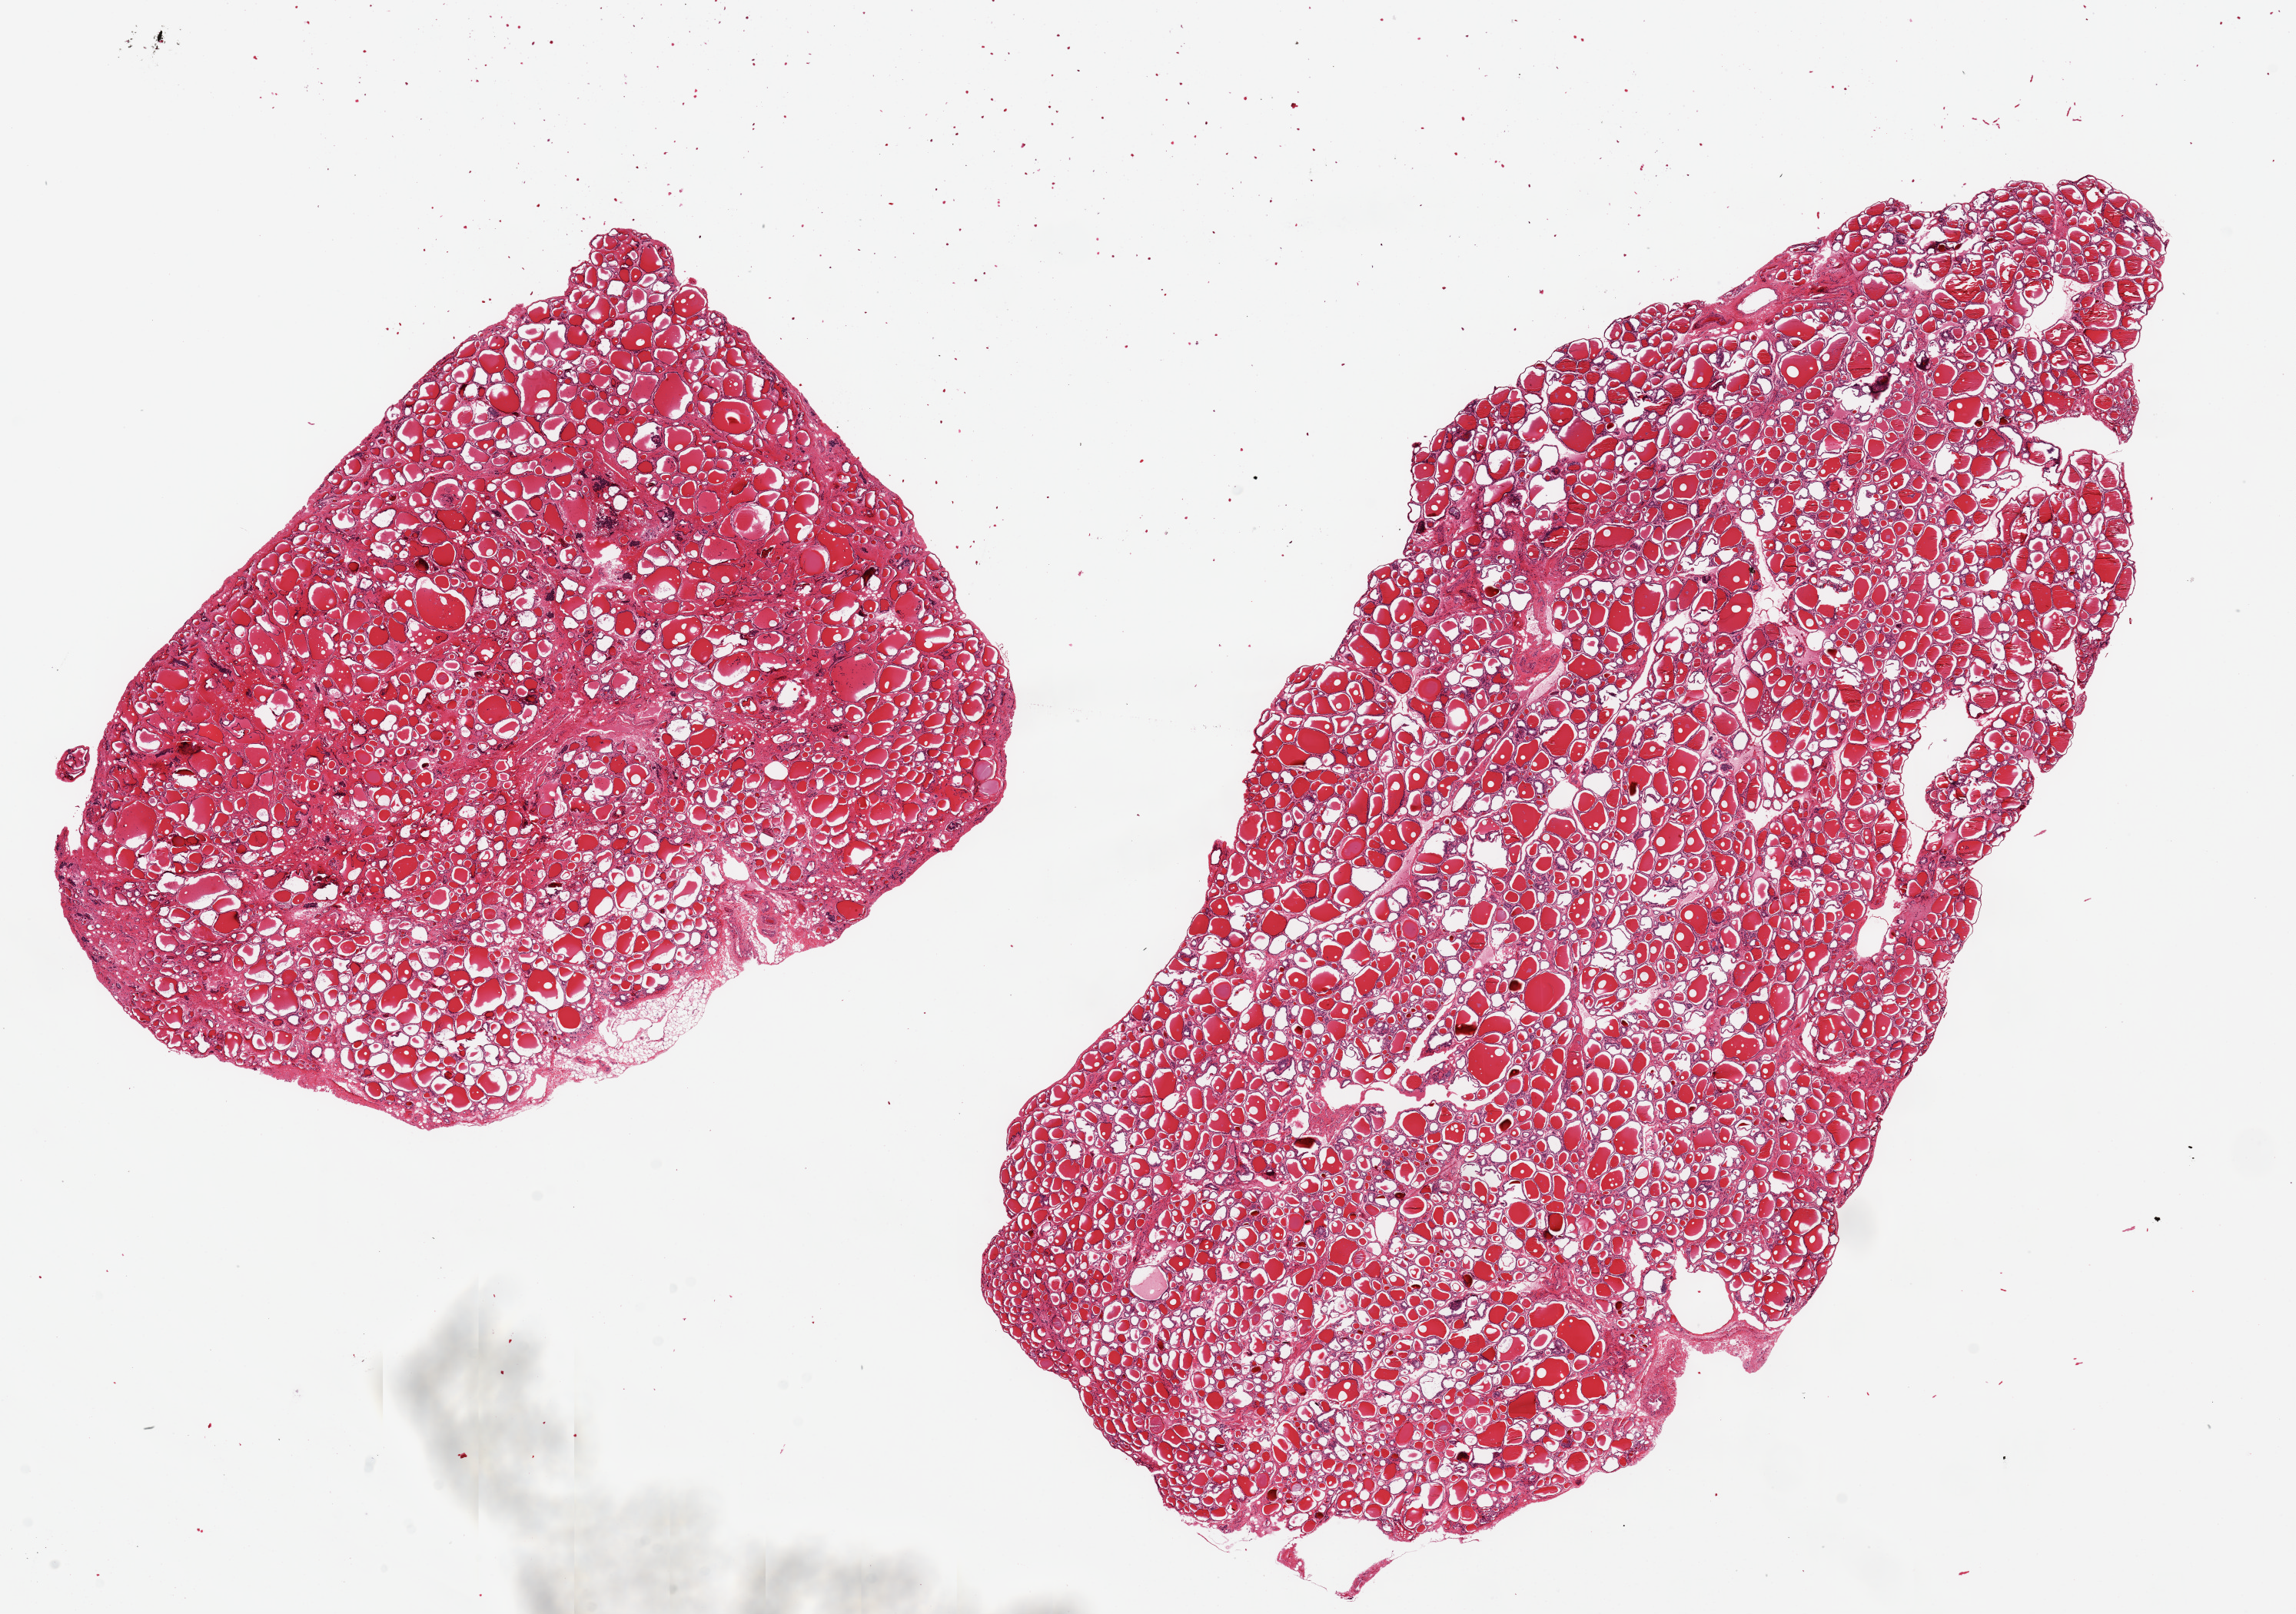
Digitized haematoxylin and eosin-stained section, brightfield, a low-resolution overview of the entire scanned area, about 23.6 x 16.6 mm (slide scanned at 20x); PAXgene-fixed, paraffin-embedded tissue; target tissue: thyroid; donor tissue sample. Donor: male.
Reviewer comment on this tissue sample: 2 pieces ~13x7mm less well preserved than usual.